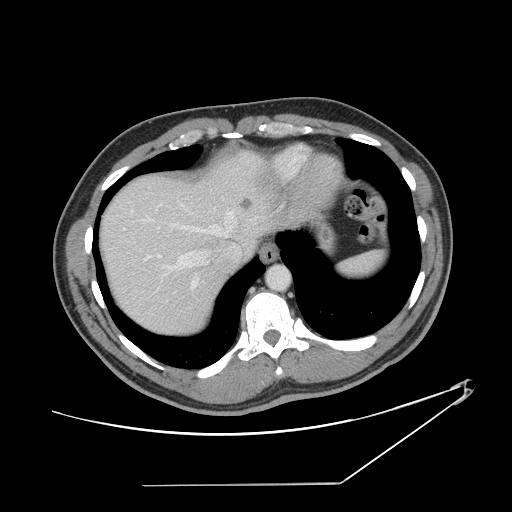
Contrast-enhanced abdominal CT, one axial slice. Reconstruction kernel STANDARD. 120 kVp. Intravenous contrast given. Soft-tissue window (W 400 / L 40 HU). 512 × 512 image matrix. Male patient, age 45 years. From the clinical record (not read from this slice): diagnosis: colorectal cancer liver metastases, imaged before liver resection; multiple liver metastases: no; largest metastasis: 1 cm; disease in both lobes: no.
Outlined on this slice (outlined manually by an expert reader):
- hepatic veins: box from (x=123, y=203) to (x=236, y=290) px
- liver: (x=102, y=153)–(x=270, y=335)
- planned liver remnant (the part of the liver to remain after resection): (x=103, y=176)–(x=234, y=334)
- portal vein (with intrahepatic branches): (x=158, y=255)–(x=161, y=257)
- liver metastasis: (x=241, y=199)–(x=254, y=208)